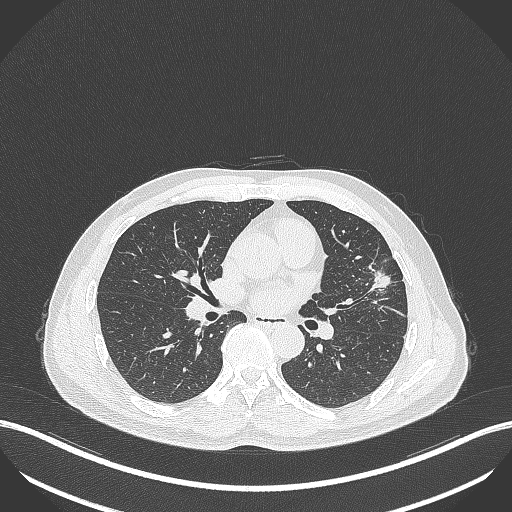
Chest CT, one axial slice. Slice 206 of 418 in the series (ordered by position). 120 kVp. Lung window (W 1500 / L -600 HU). 512 × 512 image matrix, field of view 400 × 400 mm. Patient: male, 55 years. From the clinical record (not read from this slice): clinical TNM (as recorded): T1c N0 M0; histopathological grade: G2-3.
Outlined on this slice (rectangle marked by the reading radiologist):
- lung tumour (recorded histology: adenocarcinoma): box from (x=365, y=264) to (x=395, y=292) px